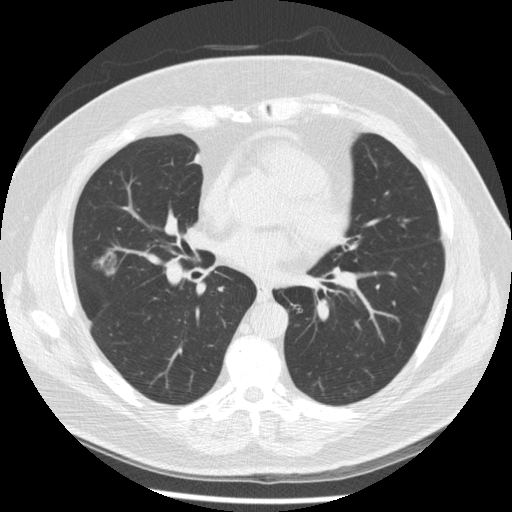
Low-dose screening chest CT, one axial slice. Position 112 of 230 along the scan axis. Reconstruction kernel STANDARD. 120 kVp. Lung window (W 1500 / L -600 HU). 2.5 mm slice thickness. 512 × 512 image matrix.
Annotated regions visible in this slice (outlined manually by an expert reader):
- lesion 1 (tumor, middle lobe of right lung): bounding box [x1, y1, x2, y2] px = [96, 250, 118, 277]